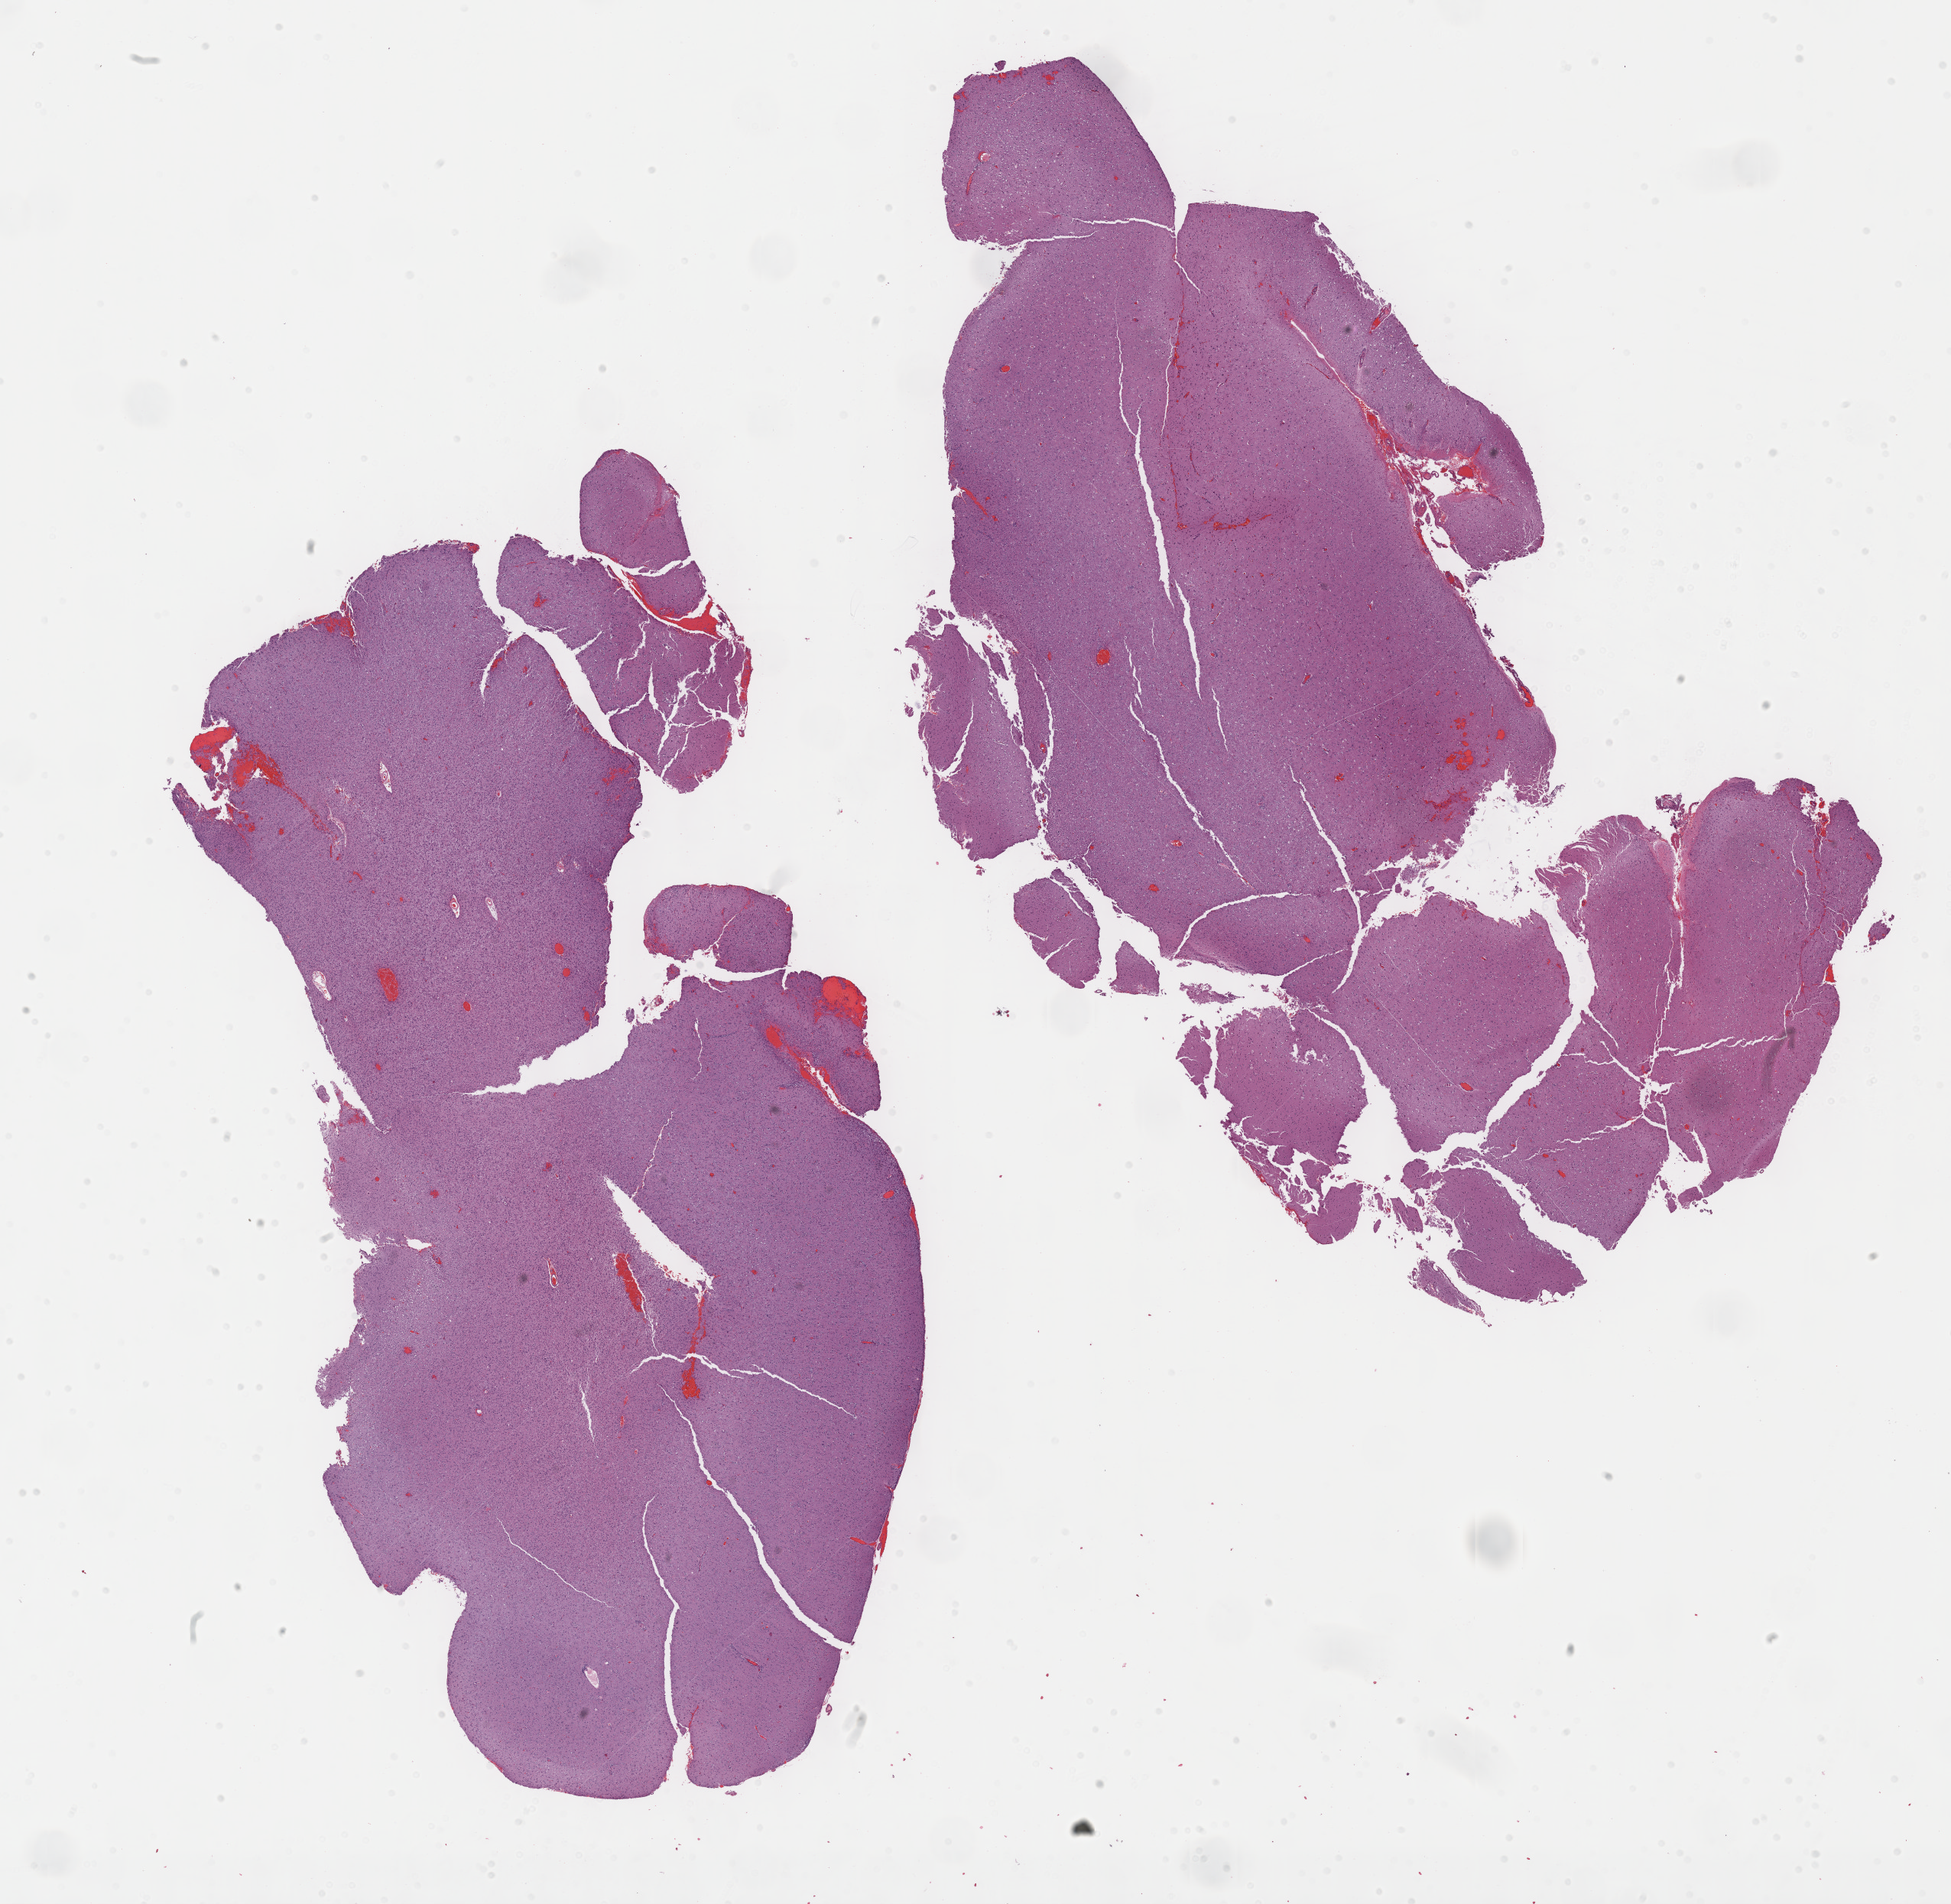
Whole-slide histology image, H&E, low-resolution overview of the scanned area, about 20.6 x 20.1 mm (slide scanned at 40x). Formalin-fixed paraffin-embedded (FFPE) diagnostic section. Primary tumour sample from the brain. Male patient; age at initial diagnosis 28 years.
Histologic diagnosis: Mixed glioma.